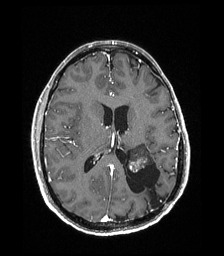
Brain MRI from a brain-tumour surgery series, one axial slice. Slice 86 of 192 in the series (ordered by position). T1-weighted post-contrast. 1 mm slice thickness. 224 × 256 image matrix, field of view 224 × 256 mm. Case-level facts recorded for this patient, not image findings: histopathology: Low grade glioma; IDH mutation: no; tumour location: Left Parieto-Occipital Intraventricular.
Annotated regions visible in this slice (expert manual segmentation):
- previous resection cavity: bounding box [x1, y1, x2, y2] px = [126, 157, 165, 207]
- tumour: [129, 144, 153, 173]